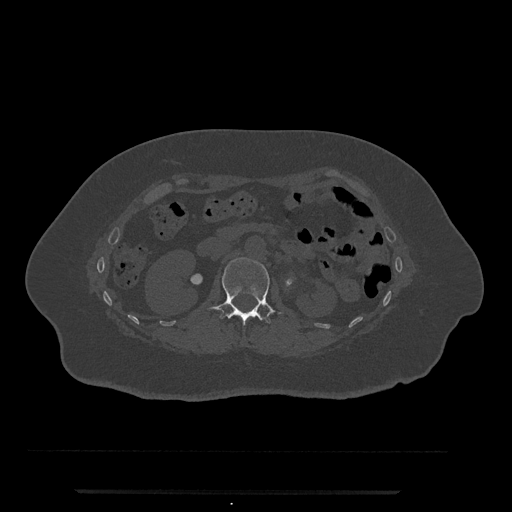
CT including the spine, one axial slice; position 103 of 797 along the scan axis; reconstruction kernel Br40s/3; bone window (W 1800 / L 400 HU); 0.5 mm slice thickness; 512 × 512 image matrix, field of view 440 × 440 mm. Patient: female, 51 years. Case-level facts recorded for this patient, not image findings: primary cancer: neuro; vertebrae with lytic lesions (as recorded): T8.
Outlined on this slice (semi-automatically segmented with operator editing):
- L1 vertebra: bounding box (x1, y1, x2, y2) in pixels: (207, 258, 282, 324)